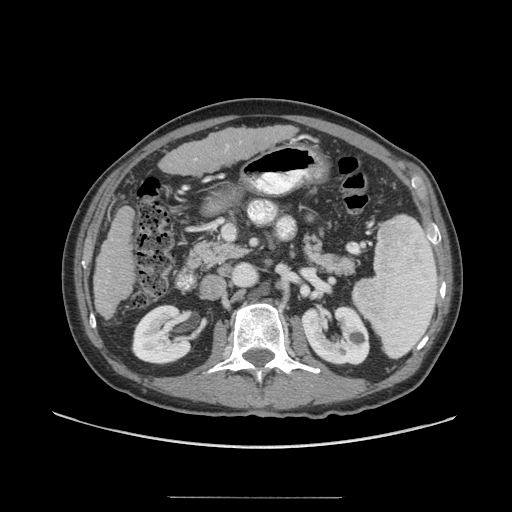
Contrast-enhanced abdominal CT (liver protocol), one axial slice; position 19 of 71 along the scan axis; 140 kVp; soft-tissue window (W 400 / L 40 HU); 2.5 mm slice thickness; 512 × 512 image matrix, field of view 400 × 400 mm. Case-level facts recorded for this patient, not image findings: diagnosis: hepatocellular carcinoma (patient treated with transarterial chemoembolisation; whether this scan precedes or follows treatment is not stated here); TNM stage (as recorded): Stage-I; Child-Pugh class: A; tumour differentiation: well differentiated; tumour nodularity: uninodular.
Annotated regions visible in this slice (semi-automatically segmented with operator editing):
- liver parenchyma outside the tumour (the mass and vessels are separate outlines, so this box may not span the whole liver): bounding box (x1, y1, x2, y2) in pixels: (94, 124, 296, 319)
- liver vessels: (226, 145, 229, 148)